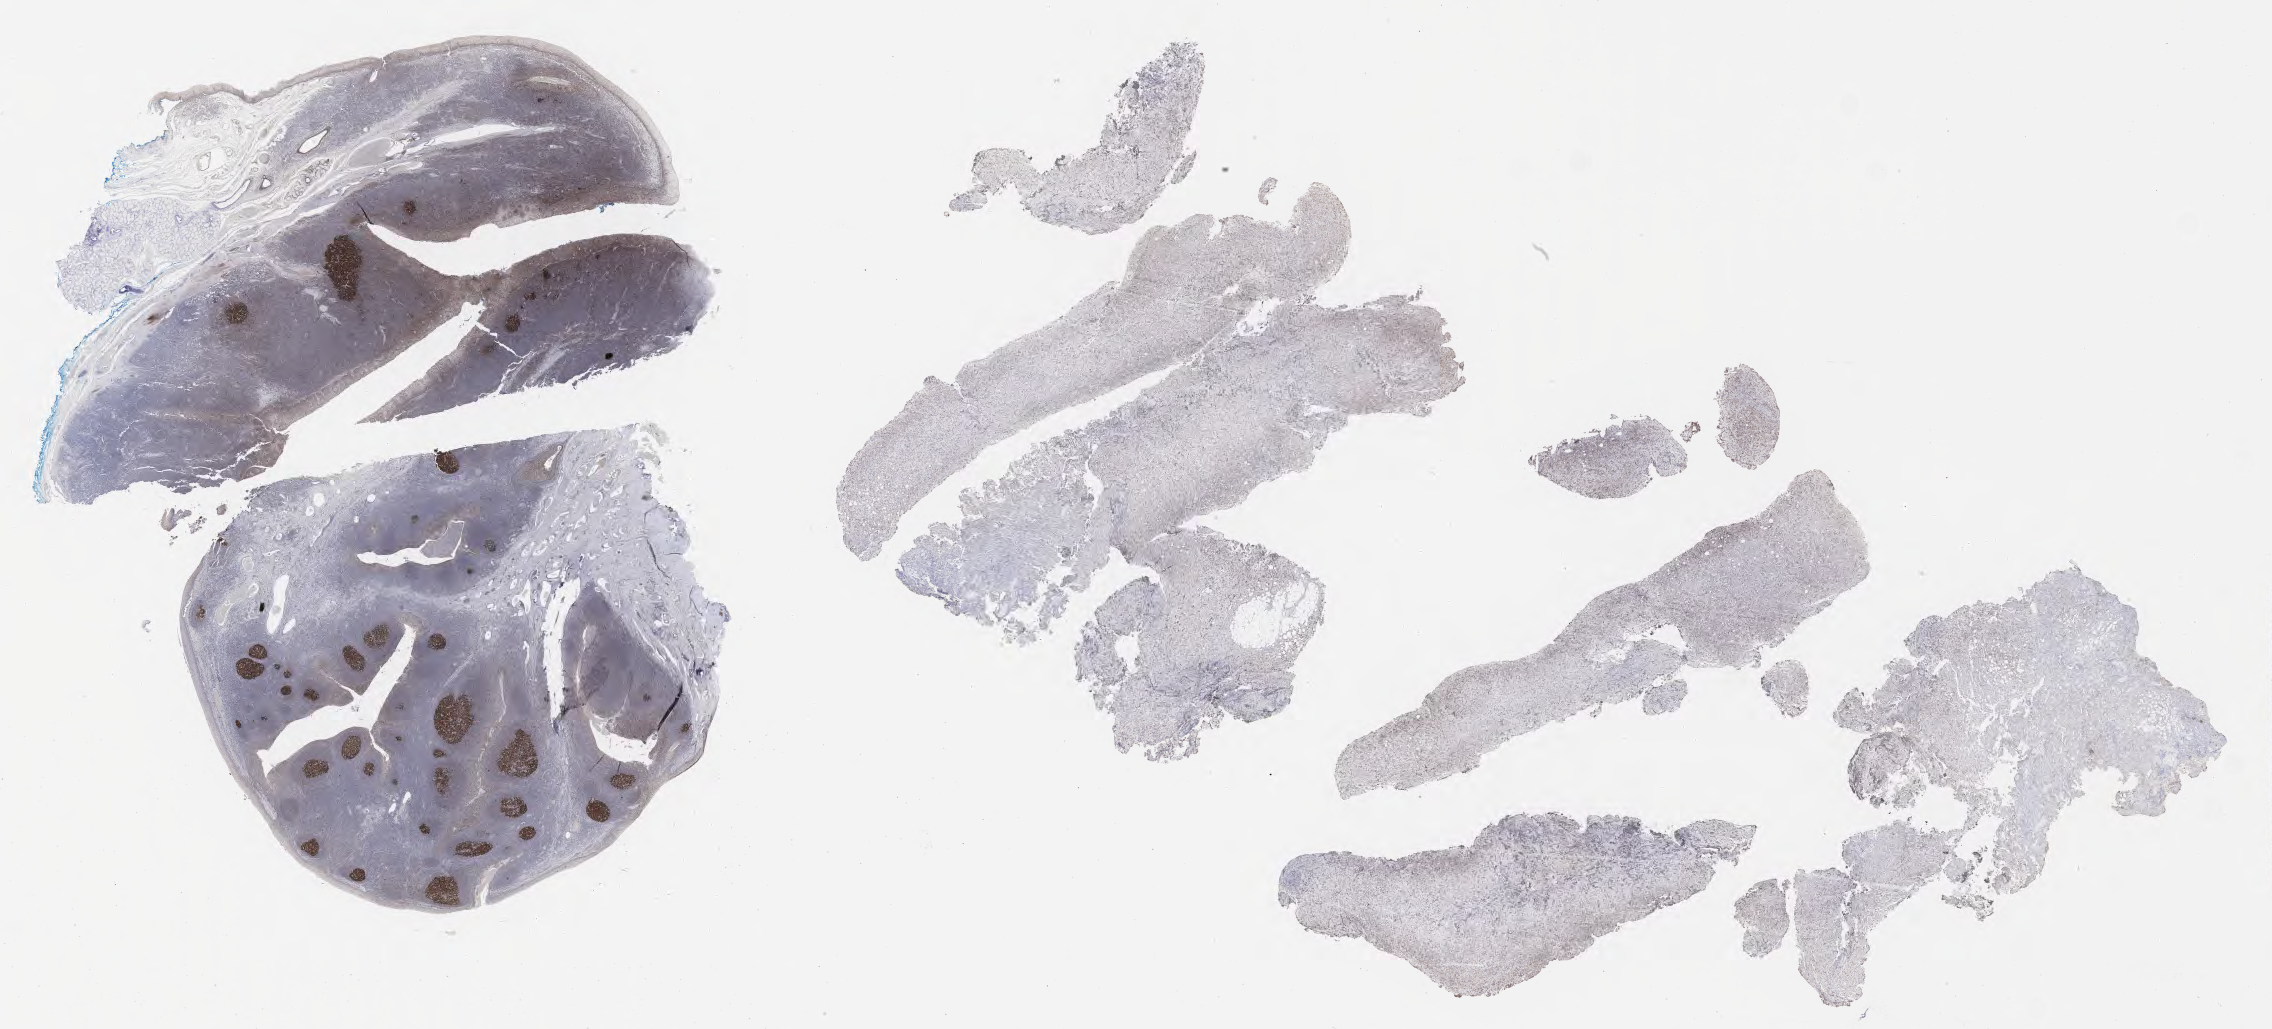
Whole-slide image, immunohistochemical stain for BCL6, a low-resolution overview of the entire scanned area, about 36.7 x 16.6 mm, tumor tissue. Patient male; 45 years old.
• histologic diagnosis: Diffuse large B-cell lymphoma, NOS